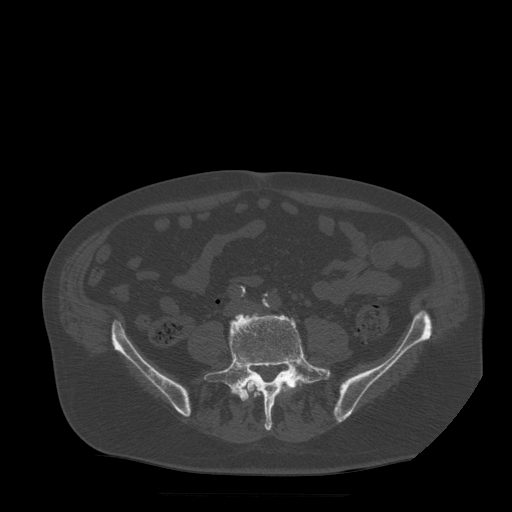
CT including the spine, one axial slice; slice 93 of 522 in the series (ordered by position); bone window (W 1800 / L 400 HU); 512 × 512 image matrix, field of view 420 × 420 mm. Patient age 72 years. Case-level facts recorded for this patient, not image findings: primary cancer: prostate.
Annotated regions visible in this slice (semi-automatic segmentation, software-assisted and operator-edited):
- L4 vertebra: bounding box [x1, y1, x2, y2] px = [243, 380, 298, 394]
- L5 vertebra: [204, 313, 332, 431]